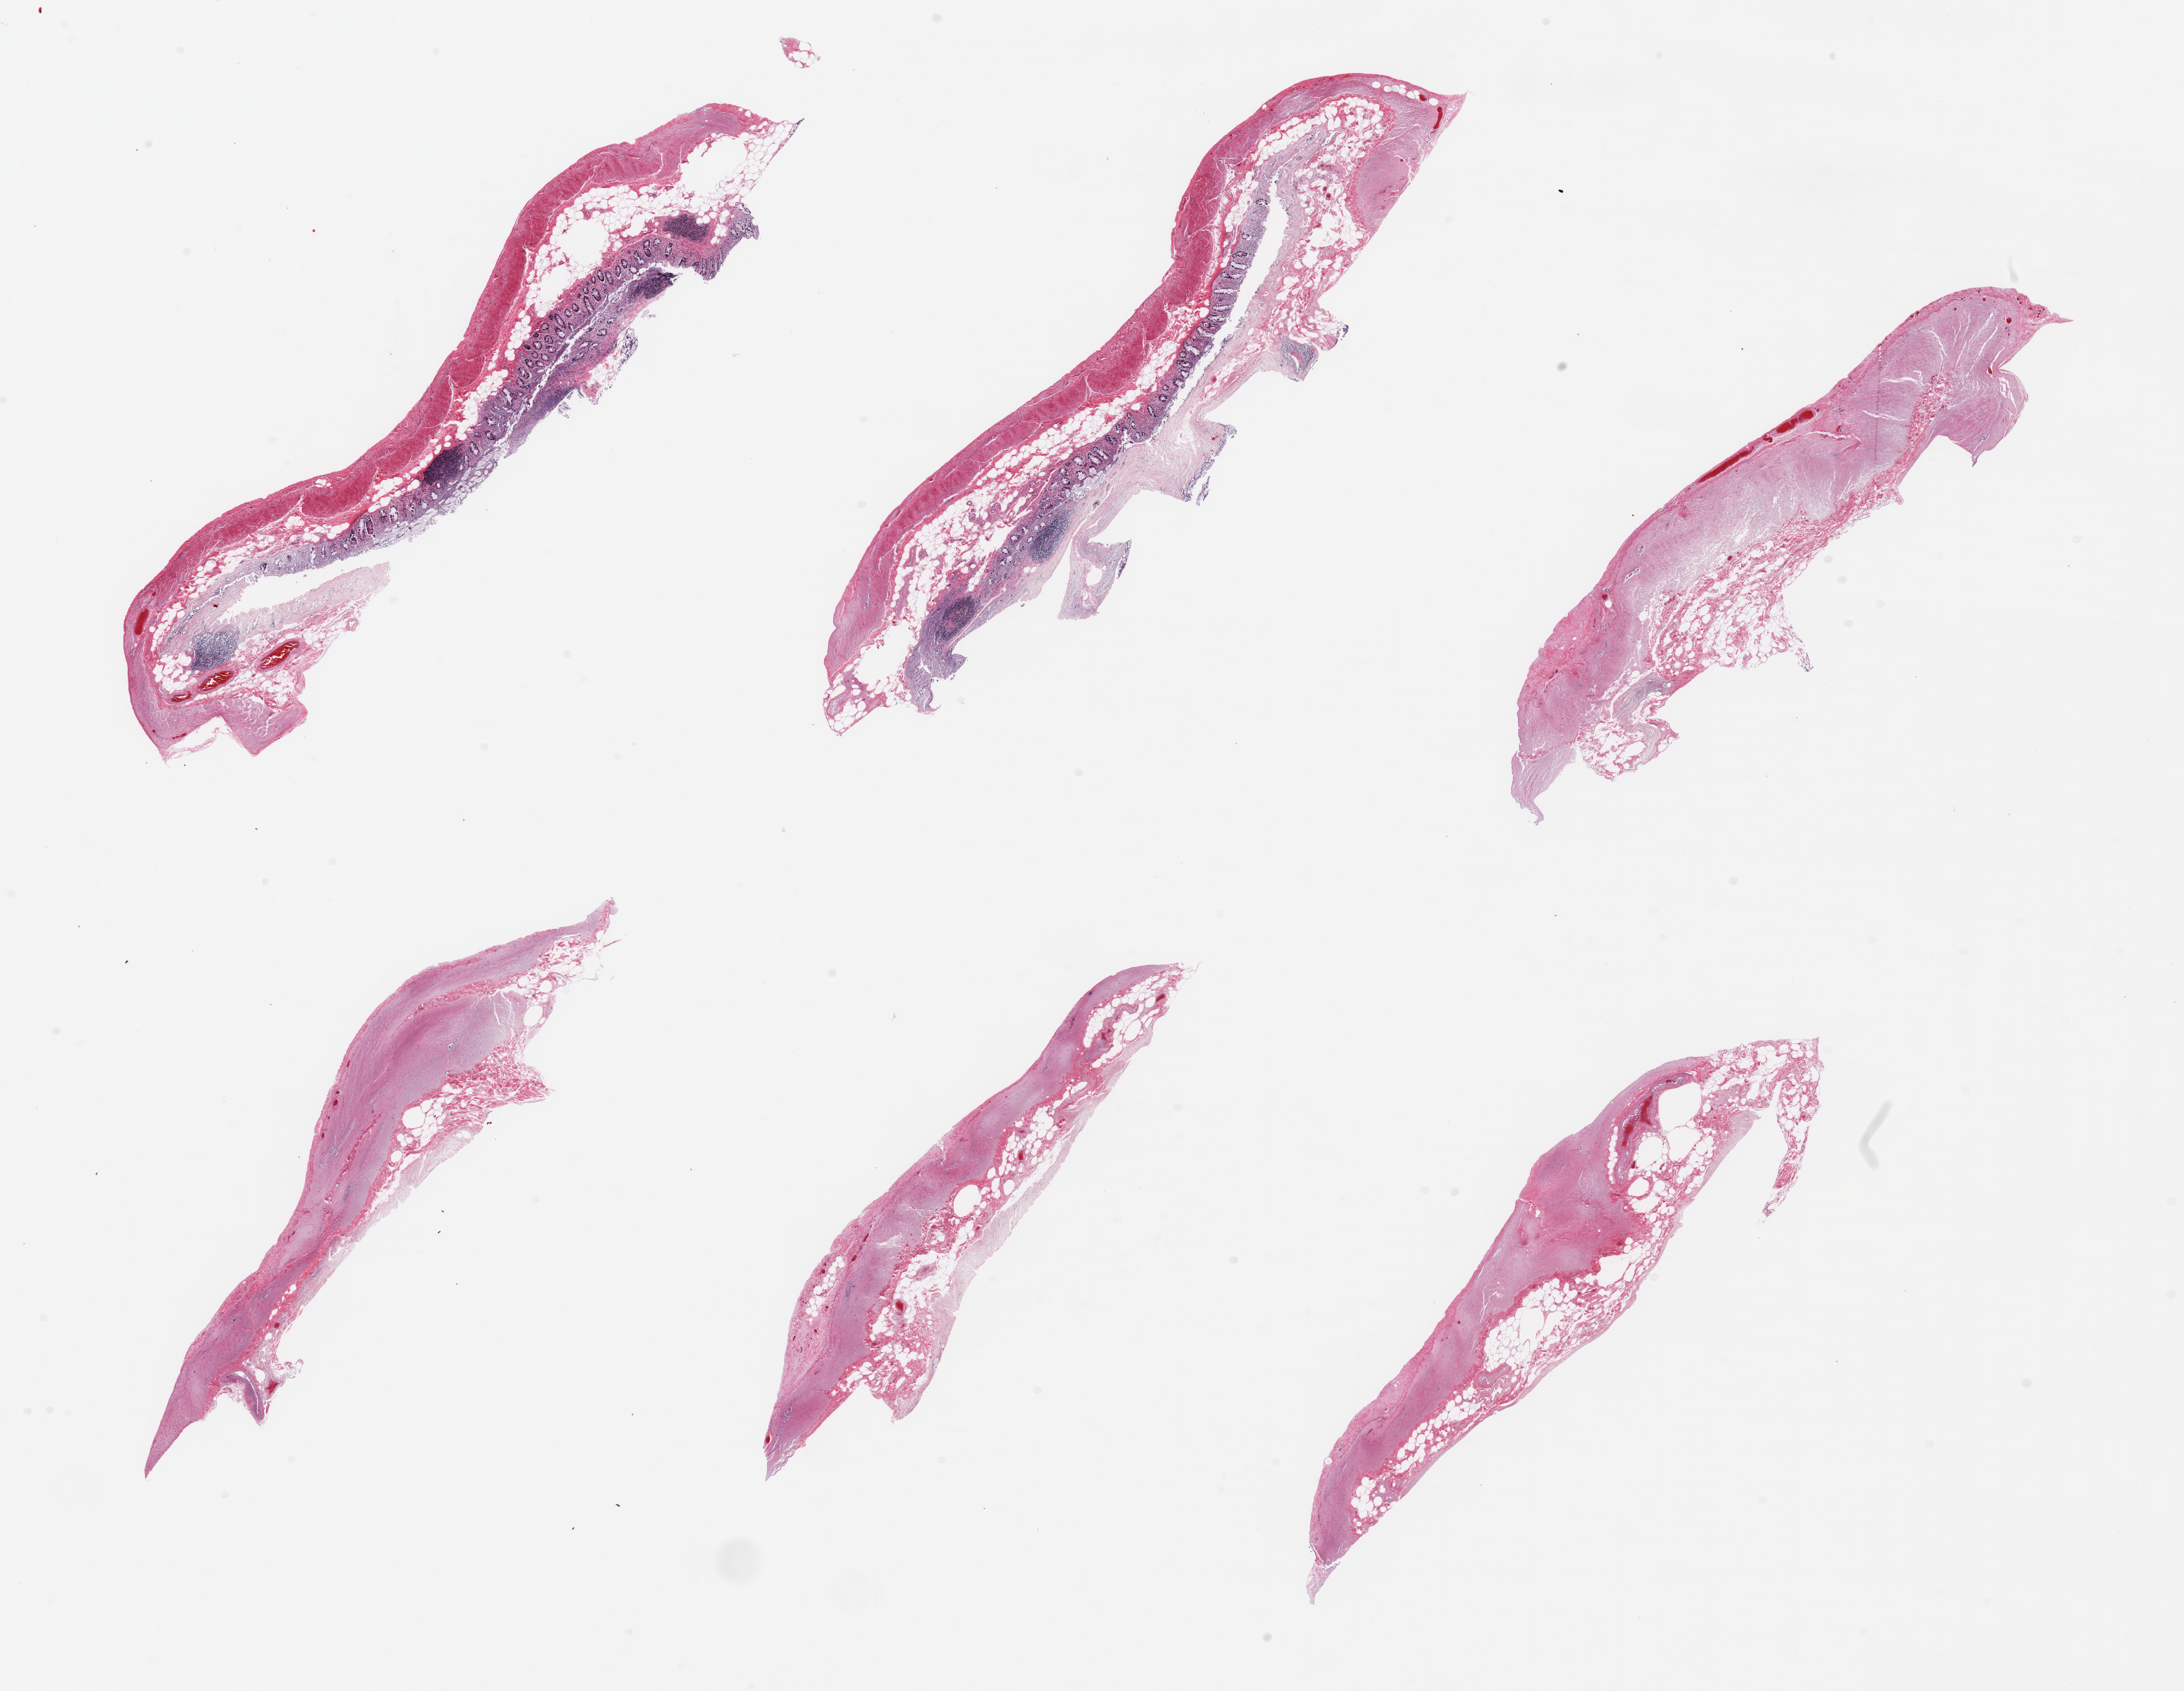
Digitized H&E-stained section — shown as a low-resolution overview of the whole scanned area (about 24.6 x 19.1 mm, acquisition: 20x scan), PAXgene-fixed paraffin-embedded (PFPE) section, target tissue: transverse colon, donor tissue sample. Donor sex: male.
• pathologist's review note for this sample: 6 pieces, target mucosa up to ~0.25mm, advanced autolysis, sloughing